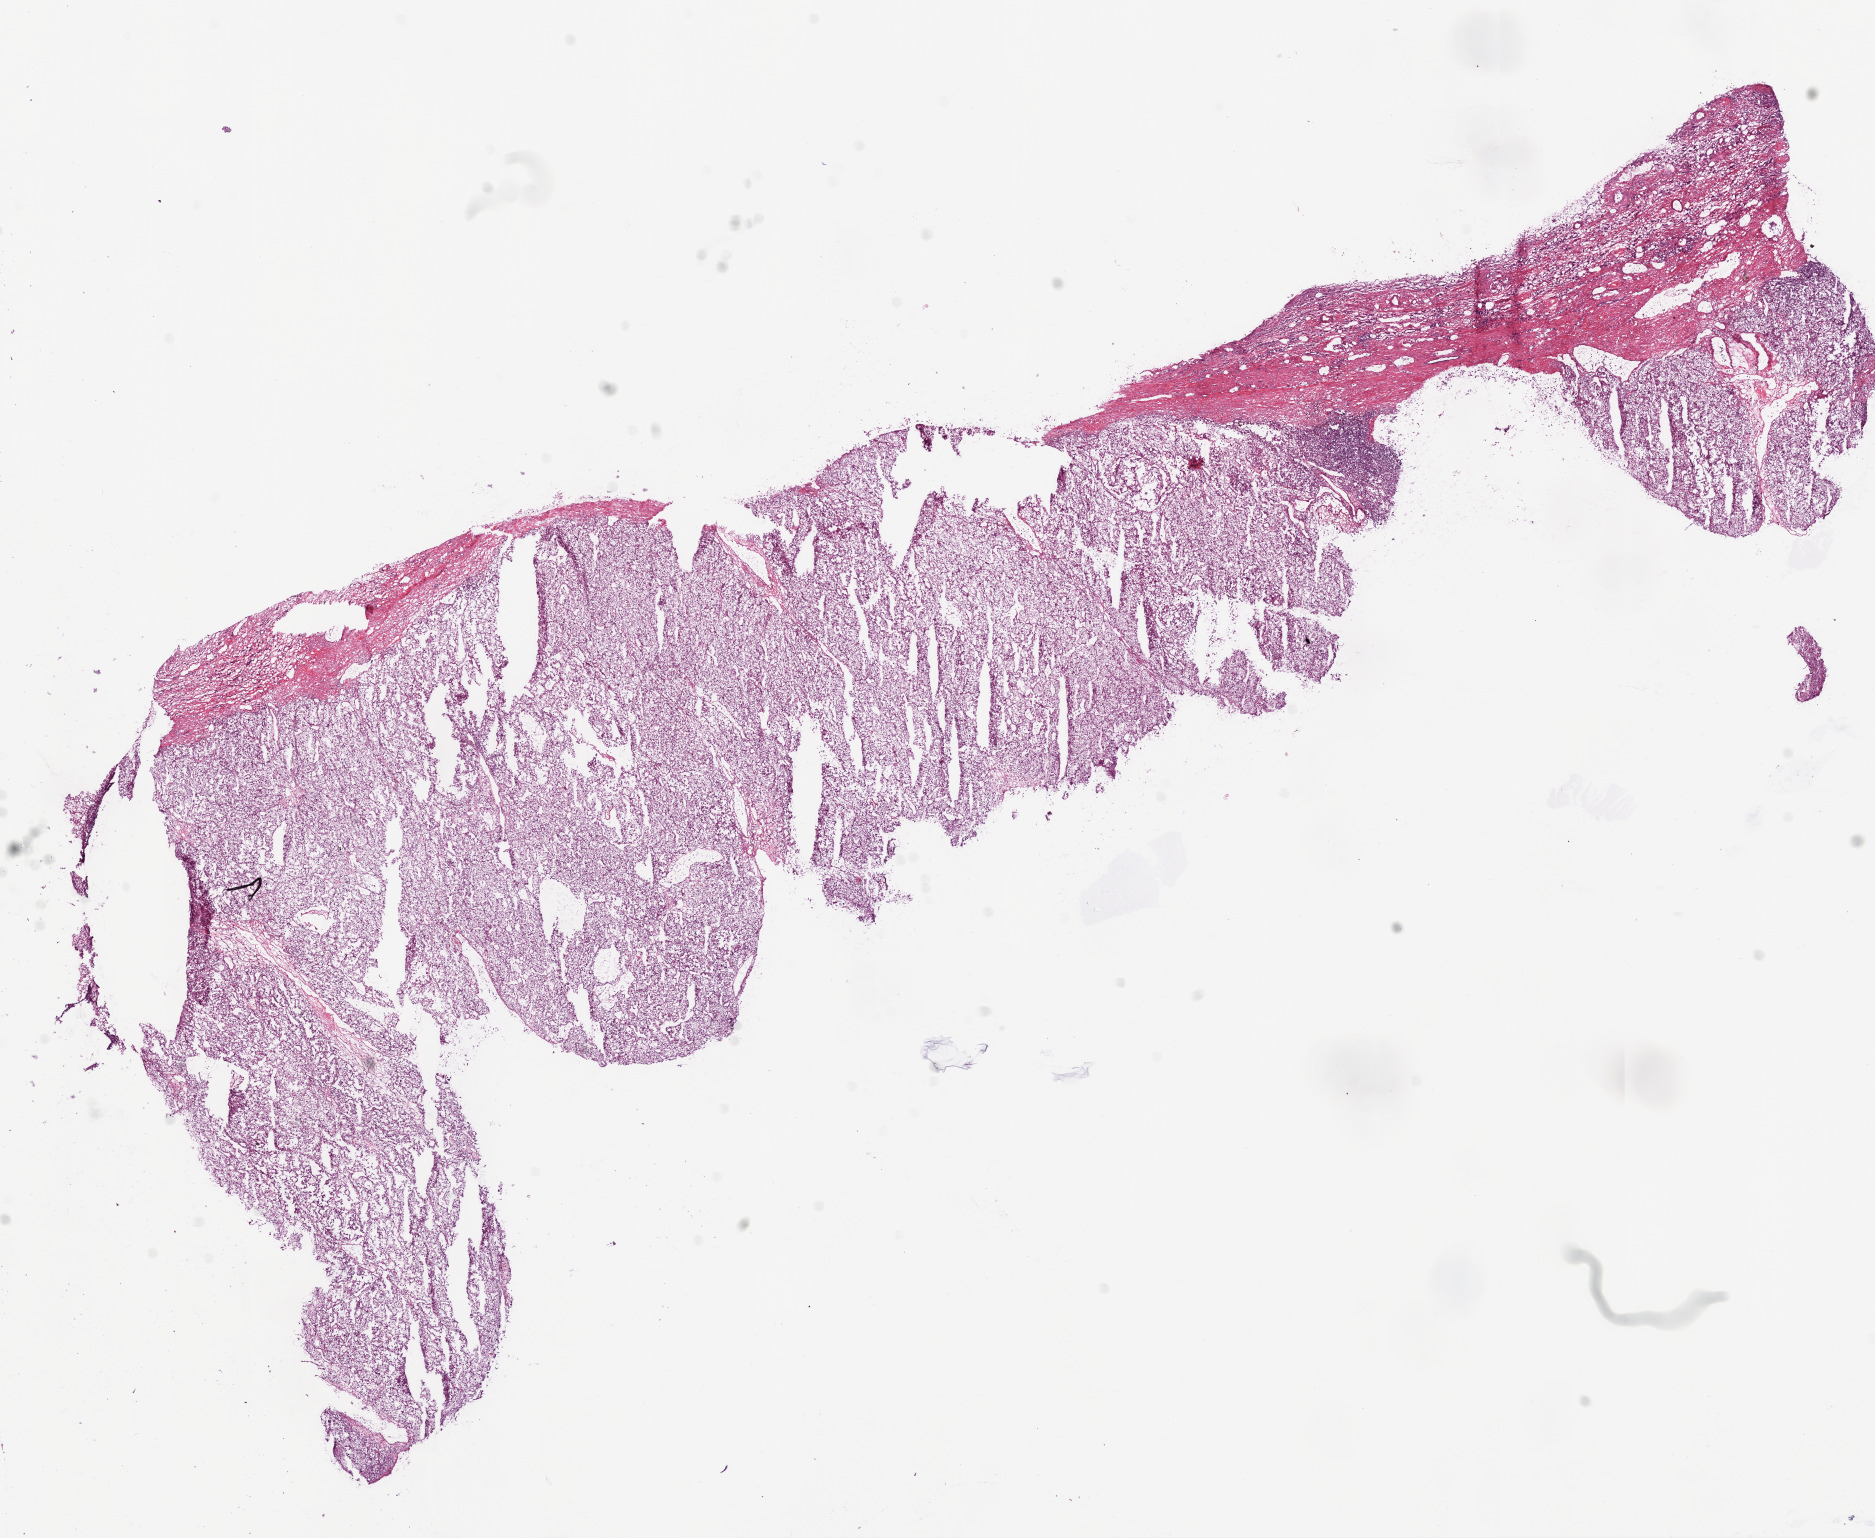
H&E-stained whole-slide image — a low-resolution overview of the entire scanned area, about 15.0 x 12.3 mm; frozen section from the bottom of the tissue portion; primary tumour sample from the kidney. Patient: female, age at initial diagnosis 60 years. Histologic grade: G3 (poorly differentiated). Pathologist review of this section (percent, as recorded): tumour cells 80%, tumour nuclei 88%, normal cells 10%, stromal cells 10%, necrosis 0%.
- TNM: T3a N0 M0
- AJCC pathologic stage: III
- pathologic diagnosis: Clear cell adenocarcinoma, NOS